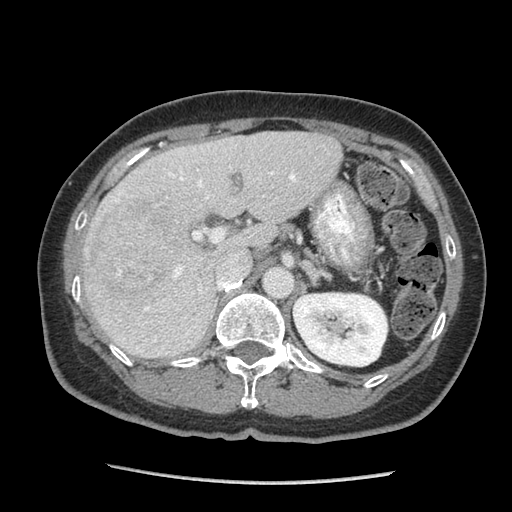
Contrast-enhanced abdominal CT (liver protocol), one axial slice; position 51 of 105 along the scan axis; reconstruction kernel STANDARD; 140 kVp; soft-tissue window (W 400 / L 40 HU); 2.5 mm slice thickness; 512 × 512 image matrix, field of view 340 × 340 mm. From the clinical record (not read from this slice): diagnosis: hepatocellular carcinoma (patient treated with transarterial chemoembolisation; whether this scan precedes or follows treatment is not stated here); TNM stage (as recorded): Stage-I; Child-Pugh class: A; tumour differentiation: moderately differentiated; tumour nodularity: uninodular.
Annotated regions visible in this slice (semi-automatic segmentation, software-assisted and operator-edited):
- liver parenchyma outside the tumour (the mass and vessels are separate outlines, so this box may not span the whole liver): bounding box (x1, y1, x2, y2) in pixels: (82, 132, 342, 358)
- mass: (85, 200, 188, 300)
- liver vessels: (115, 147, 296, 354)